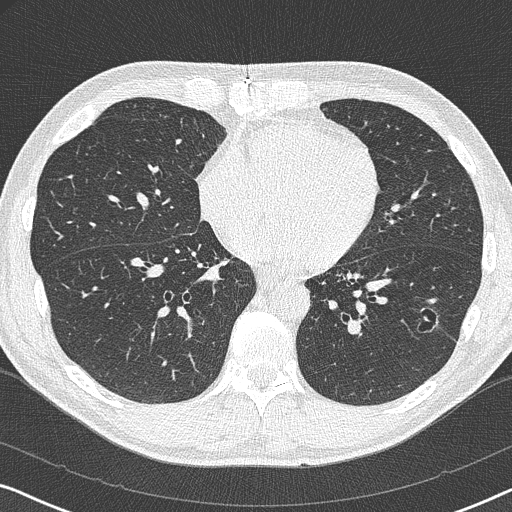
Low-dose screening chest CT, axial slice. Baseline annual screen. Lung window (W 1500 / L -600 HU). 120 kVp. Slice 207 of 327 in the series. 512 × 512 image matrix, field of view 330 × 330 mm. Male, age 59 years at enrolment.
Expert-annotated lung lesion, bounding box [x1, y1, x2, y2] px = [412, 302, 451, 338]. The screening reader recorded 2 non-calcified nodules or masses ≥4 mm on this exam (left lower lobe, right middle lobe); which of them this box marks is not recorded.